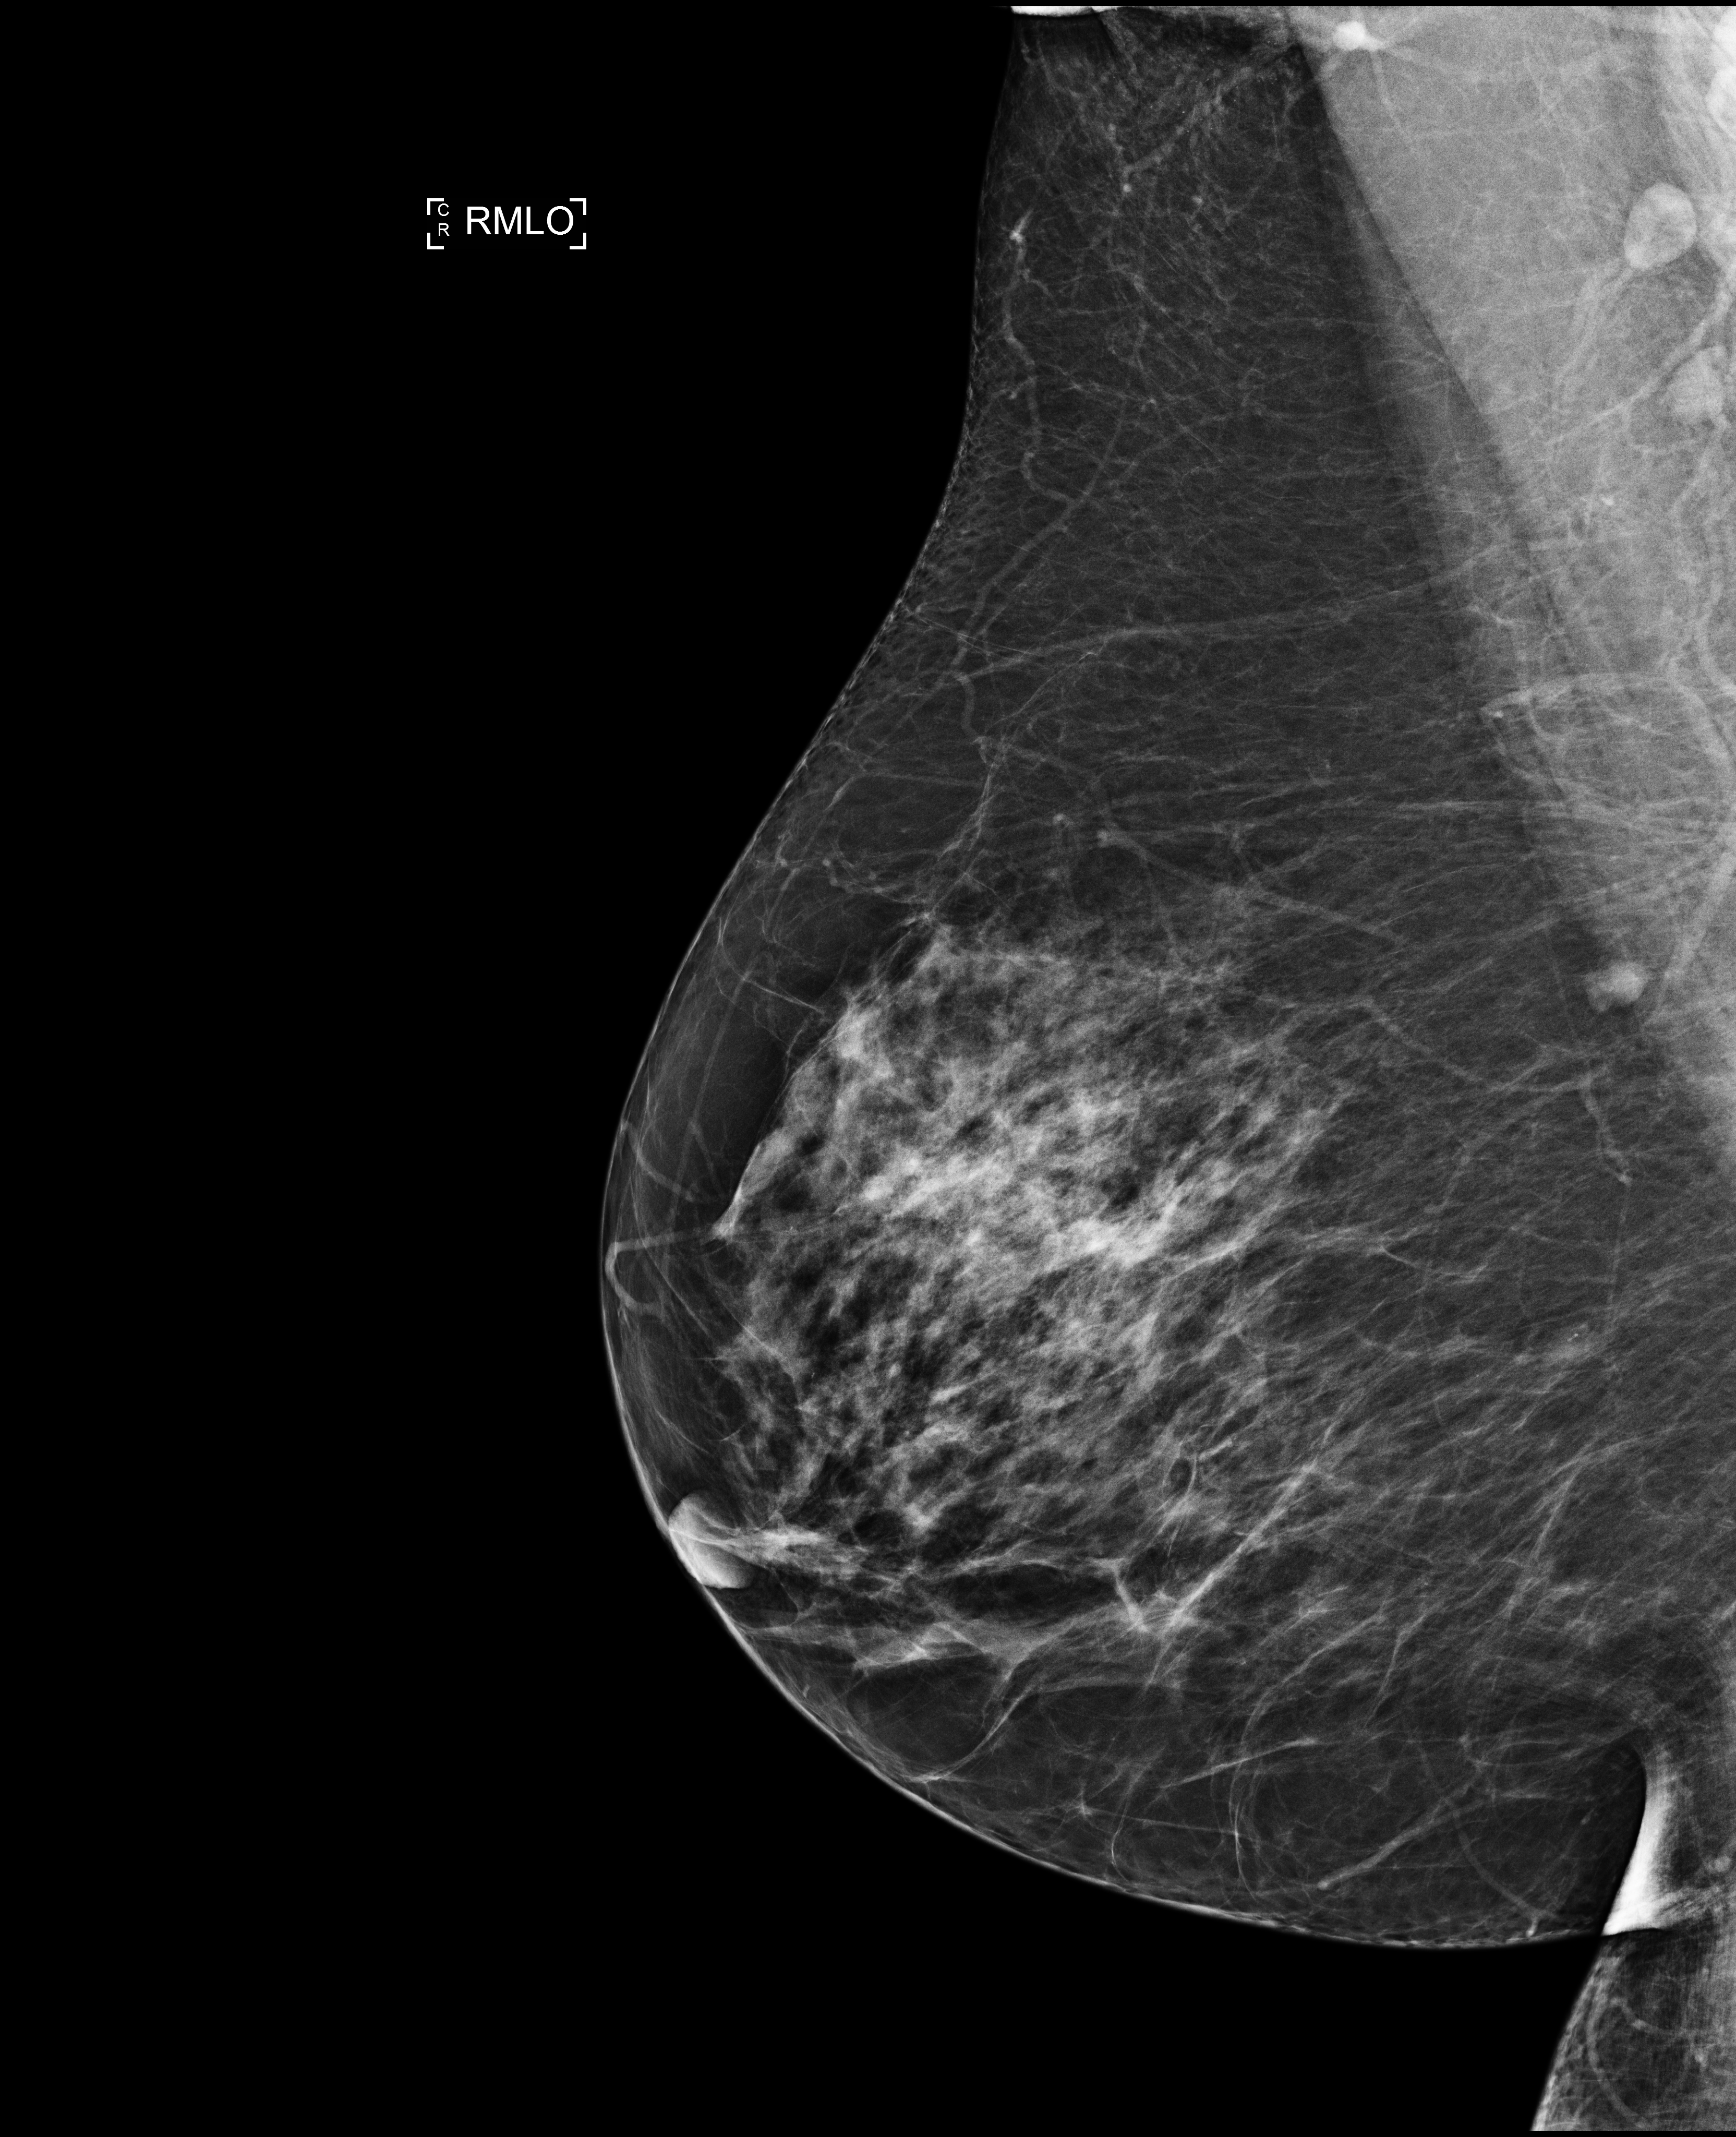
Annual screening mammography examination; system: Selenia Dimensions. Patient: female, 58 years.
Image type: full-field digital mammogram. Breast: right. Projection: mediolateral oblique (MLO) view.